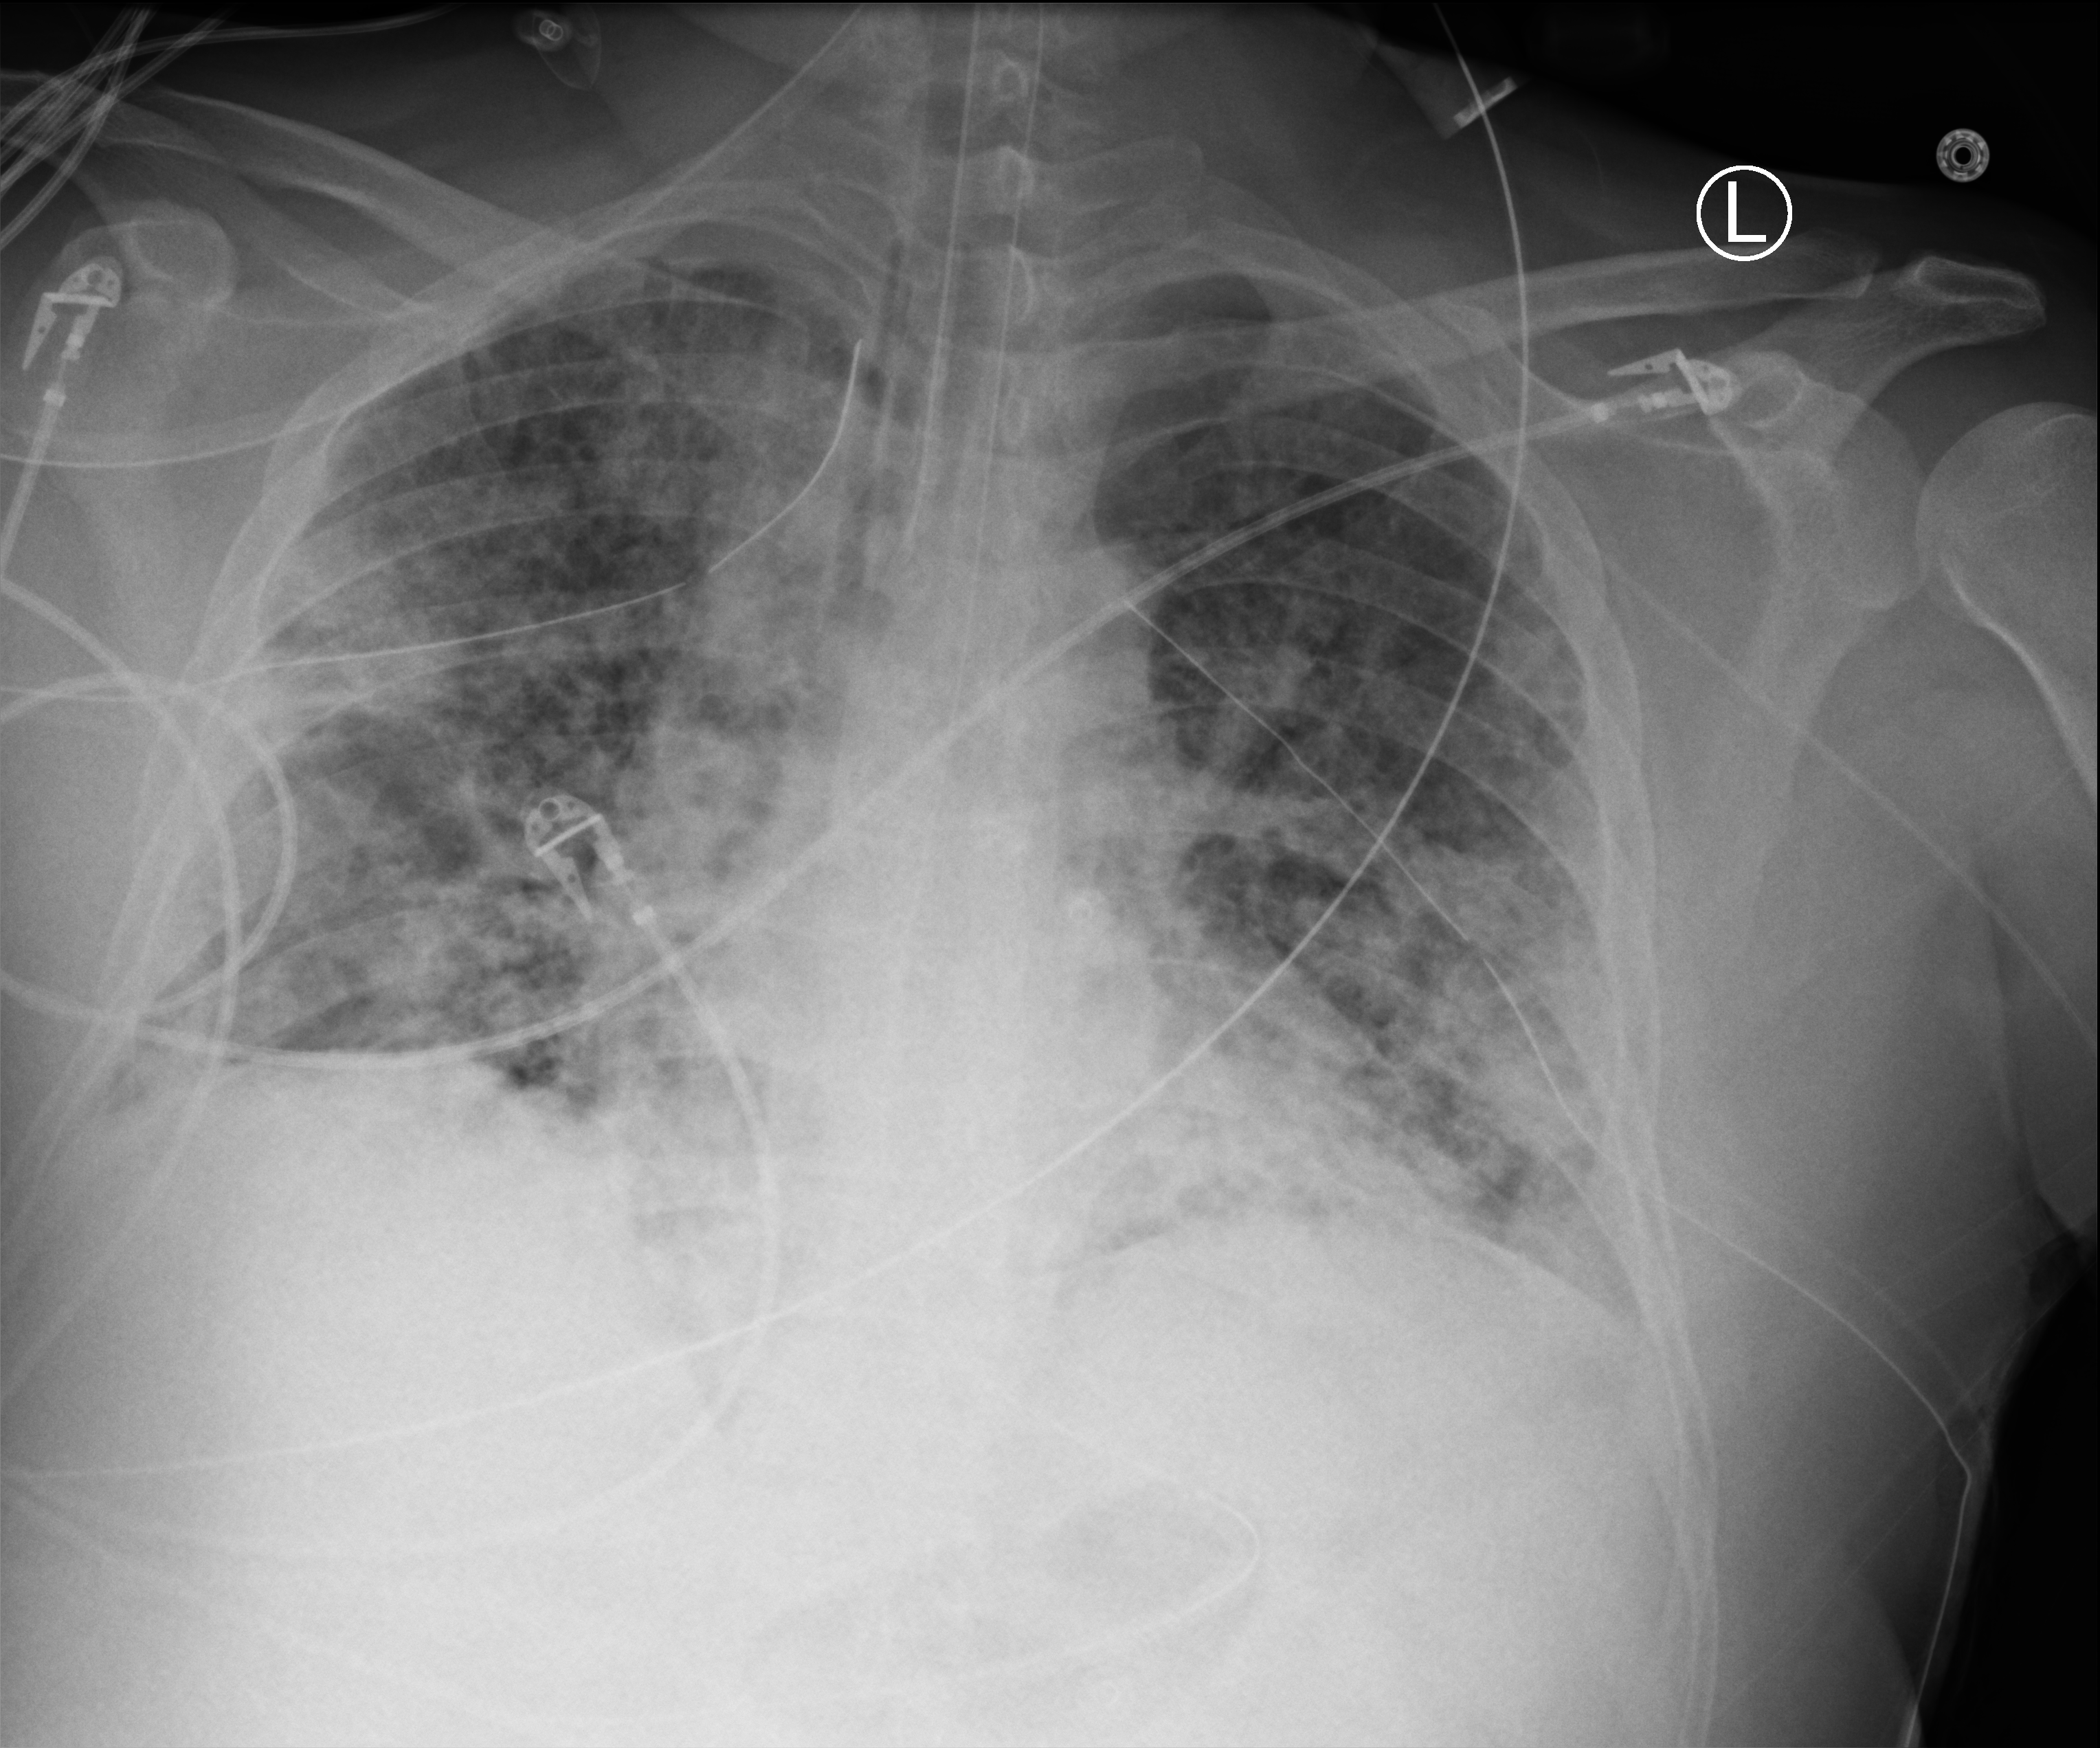
Portable chest radiograph. Patient hospitalised with COVID-19; male, aged 18–59 years.
From the hospital-stay record, not from the radiograph (when in the stay this image was taken is not recorded):
- admitted to intensive care during this hospital stay: yes
- diabetes (admission record): yes